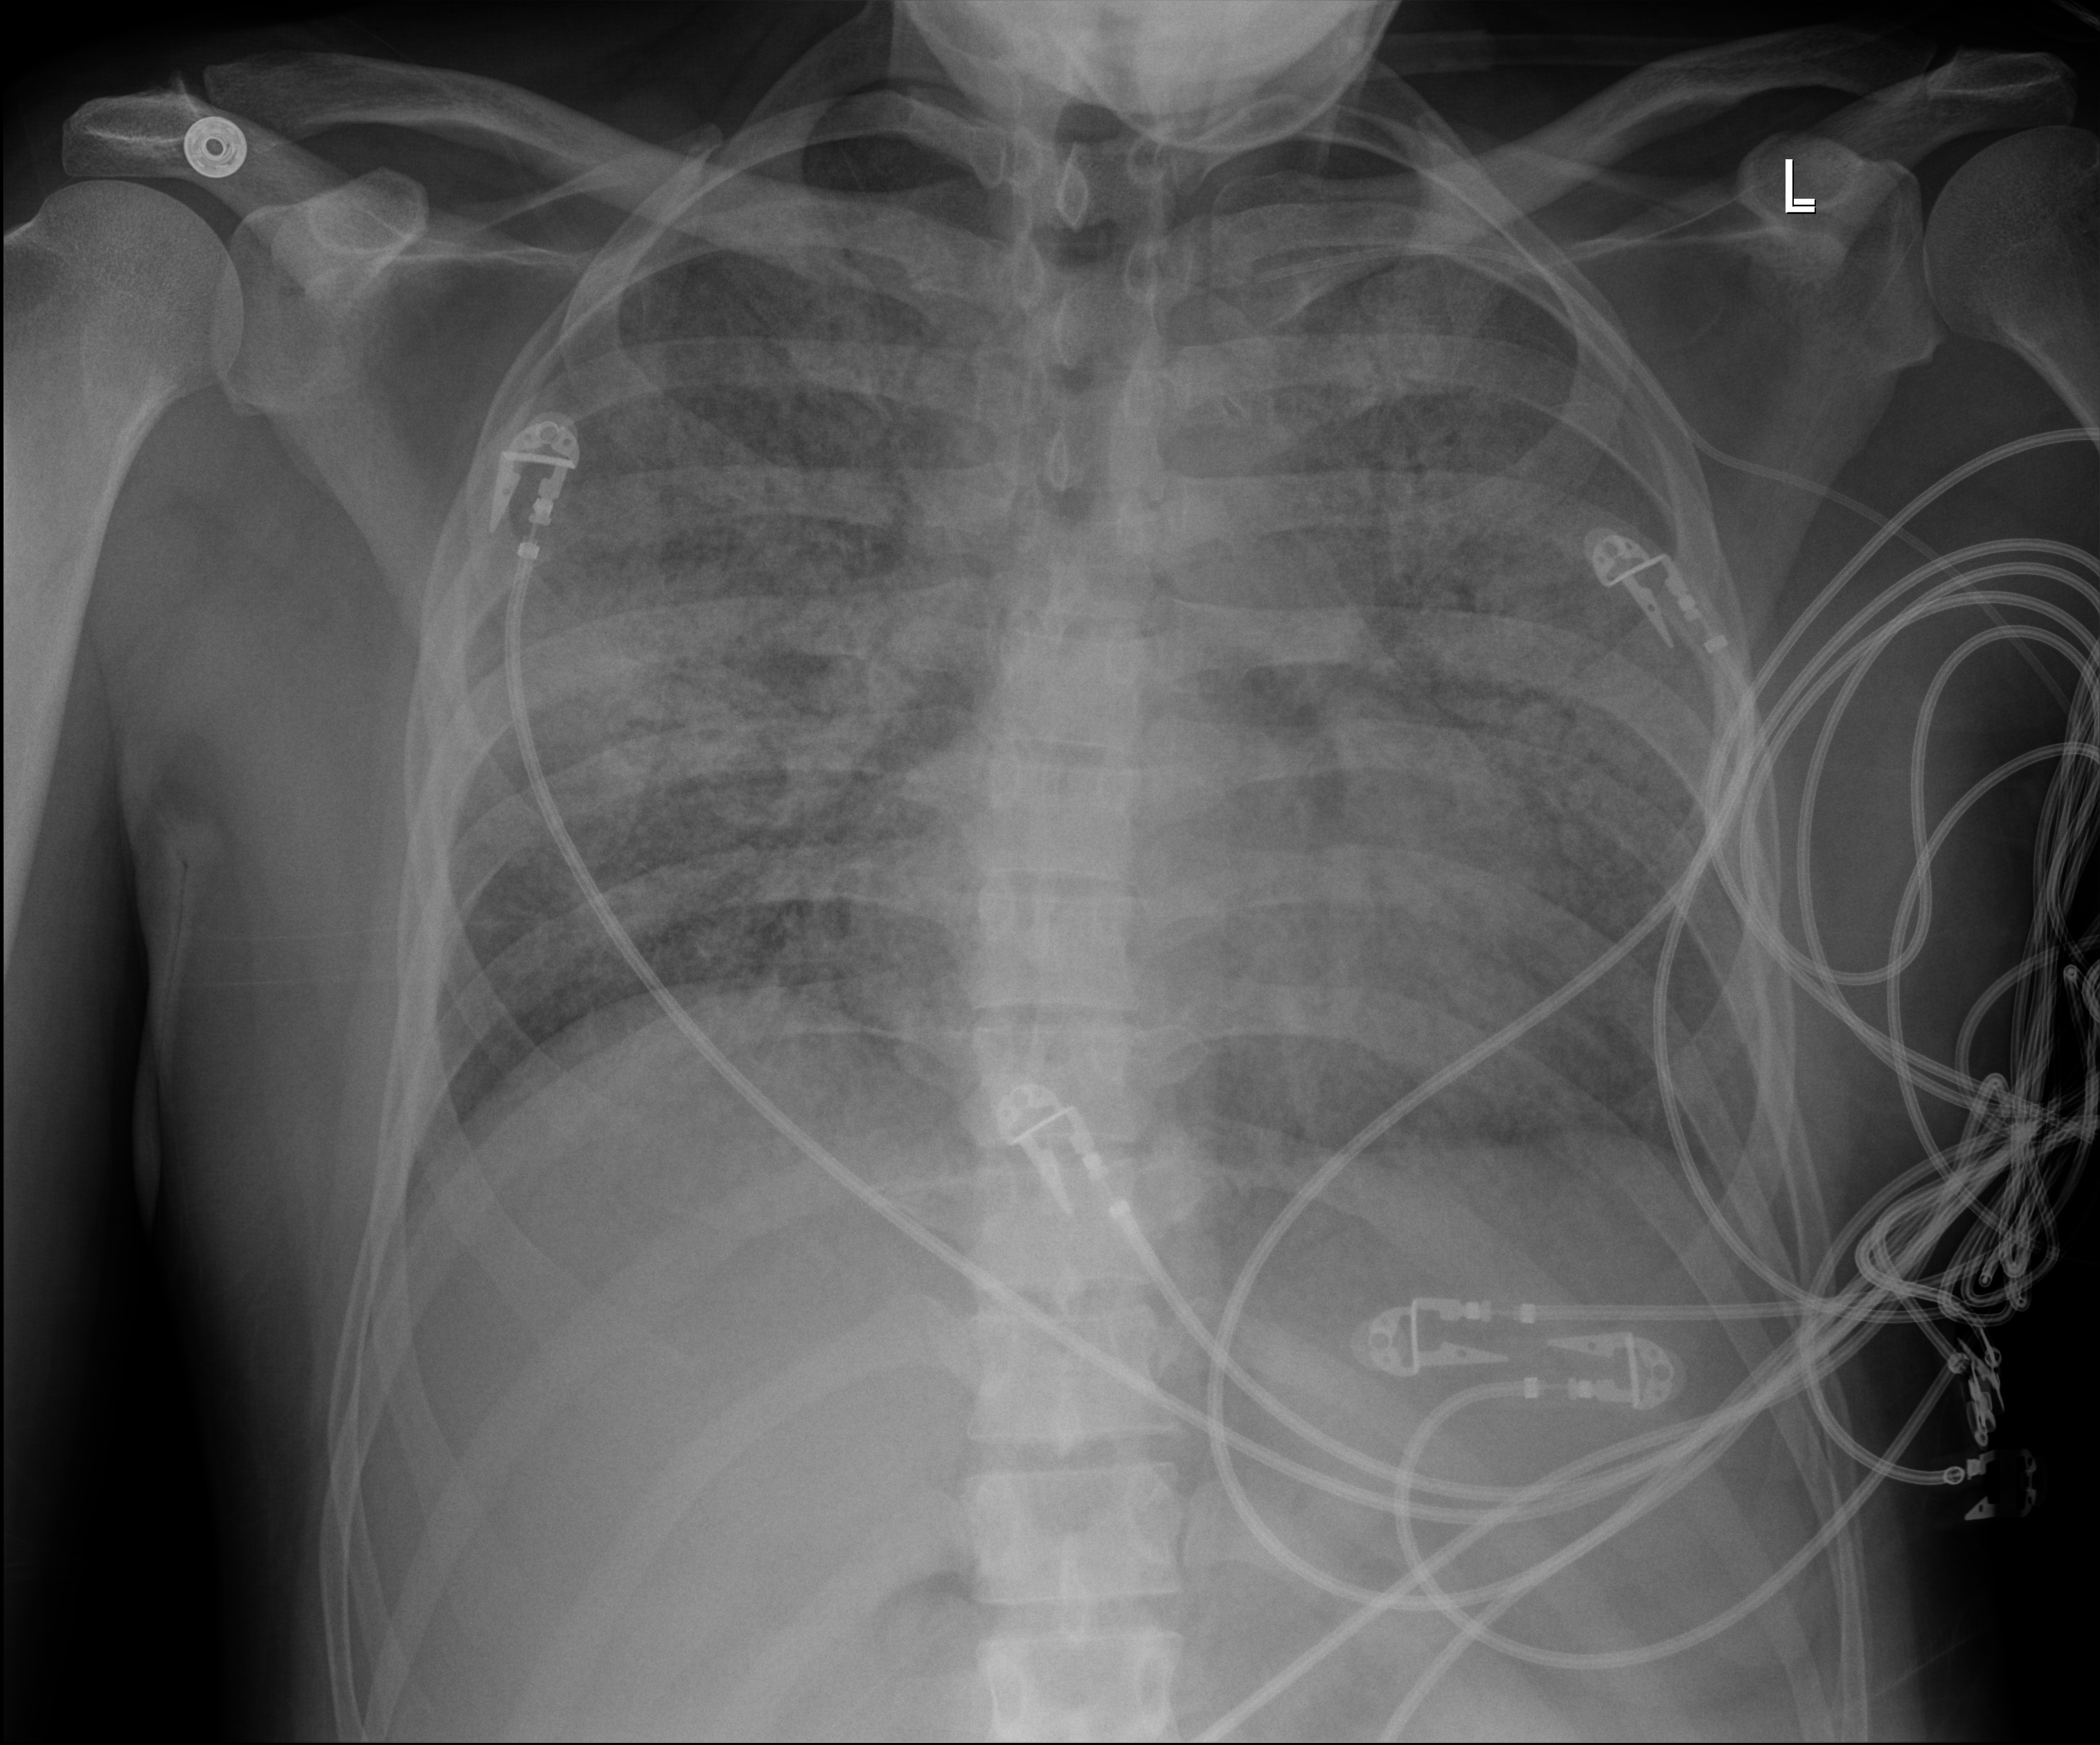
Portable chest radiograph, anteroposterior (AP) projection. Patient hospitalised with COVID-19; male, aged 18–59 years.
From the hospital-stay record, not from the radiograph (when in the stay this image was taken is not recorded):
- length of hospital stay: 30 days
- admitted to intensive care during this hospital stay: yes
- chronic kidney disease (admission record): no